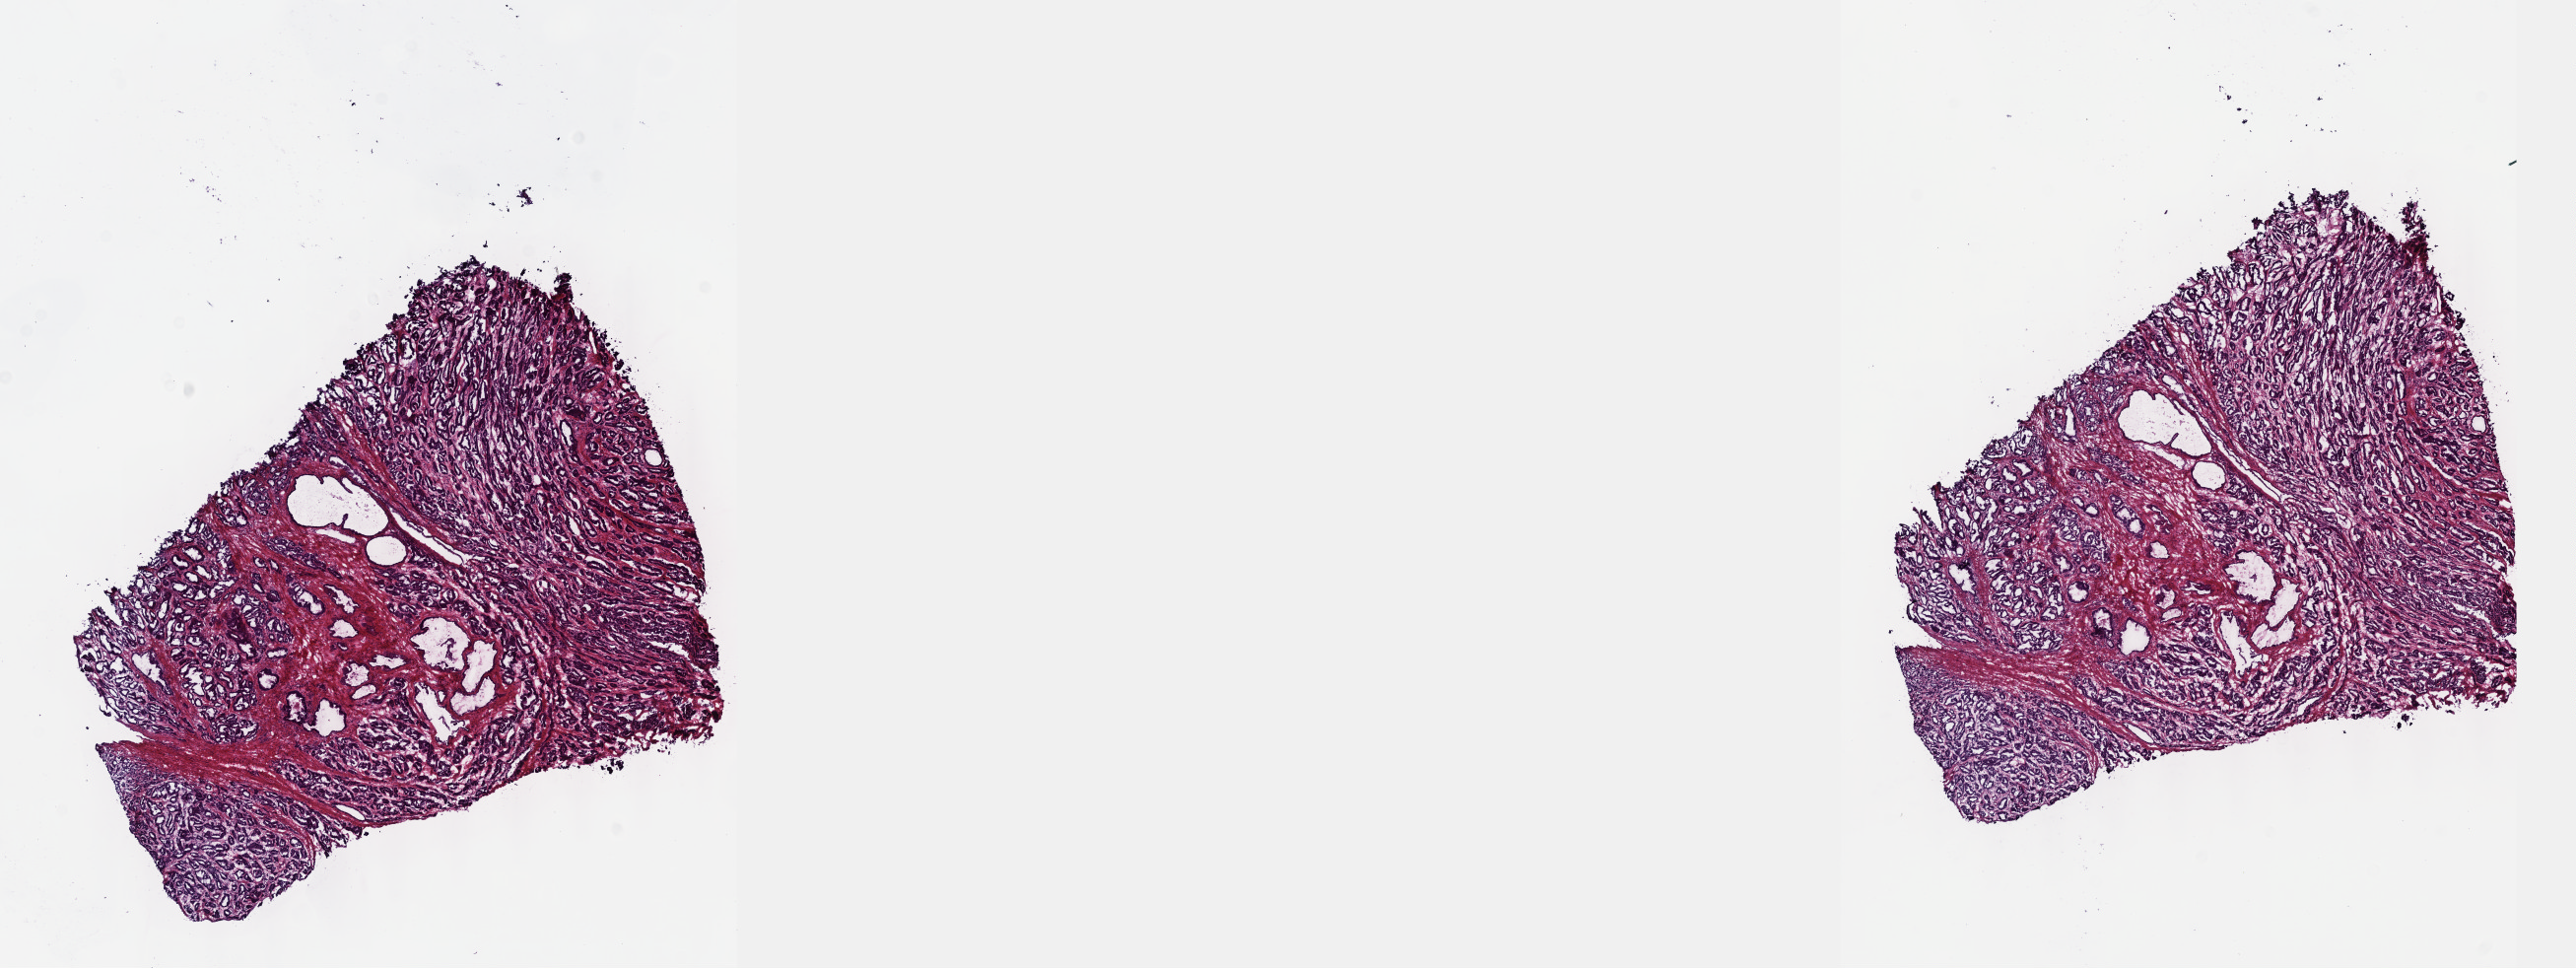
Whole-slide histology image, H&E-stained, shown as a low-resolution overview of the whole scanned area (about 21.1 x 7.9 mm). Frozen section from the top of the tissue portion. Primary tumour sample from the prostate. Male patient; age at initial diagnosis 70 years. Gleason score: 8 (4+4). Pathologist review of this section (percent, as recorded): tumour cells 85%, tumour nuclei 95%, normal cells 5%, stromal cells 10%, necrosis 0%. Infiltration values recorded for this section: lymphocyte infiltration 0%, monocyte infiltration 0%, neutrophil infiltration 0%.
- lymph nodes positive (case pathology): 0 of 4 examined
- laterality: bilateral
- pathologic diagnosis: Adenocarcinoma, NOS (prostate gland)